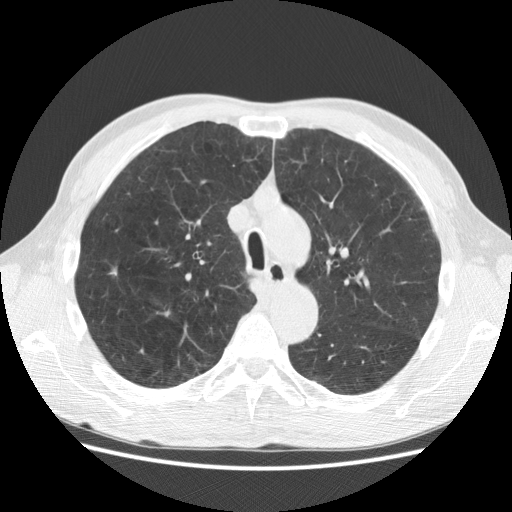
Low-dose screening chest CT, one axial slice. Slice 208 of 282 in the series (ordered by position). Lung window (W 1500 / L -600 HU). 512 × 512 image matrix, field of view 367 × 367 mm.
Annotated regions visible in this slice (manually delineated by an expert):
- lesion 1 (tumor, upper lobe of right lung): bounding box (x1, y1, x2, y2) in pixels: (110, 271, 117, 275)